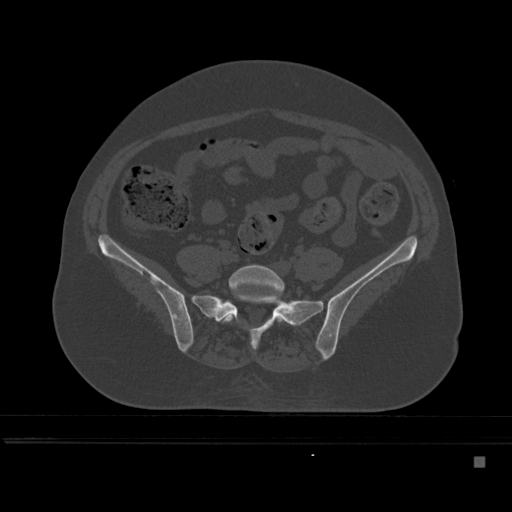
CT including the spine, one axial slice; slice 100 of 495 in the series (ordered by position); bone window (W 1800 / L 400 HU); 1.5 mm slice thickness; 512 × 512 image matrix, field of view 404 × 404 mm. Female patient, age 33 years. Case-level facts recorded for this patient, not image findings: primary cancer: breast; vertebrae with lytic lesions (as recorded): T1.
Outlined on this slice (semi-automatic segmentation, software-assisted and operator-edited):
- L5 vertebra: bounding box (x1, y1, x2, y2) in pixels: (220, 264, 285, 324)